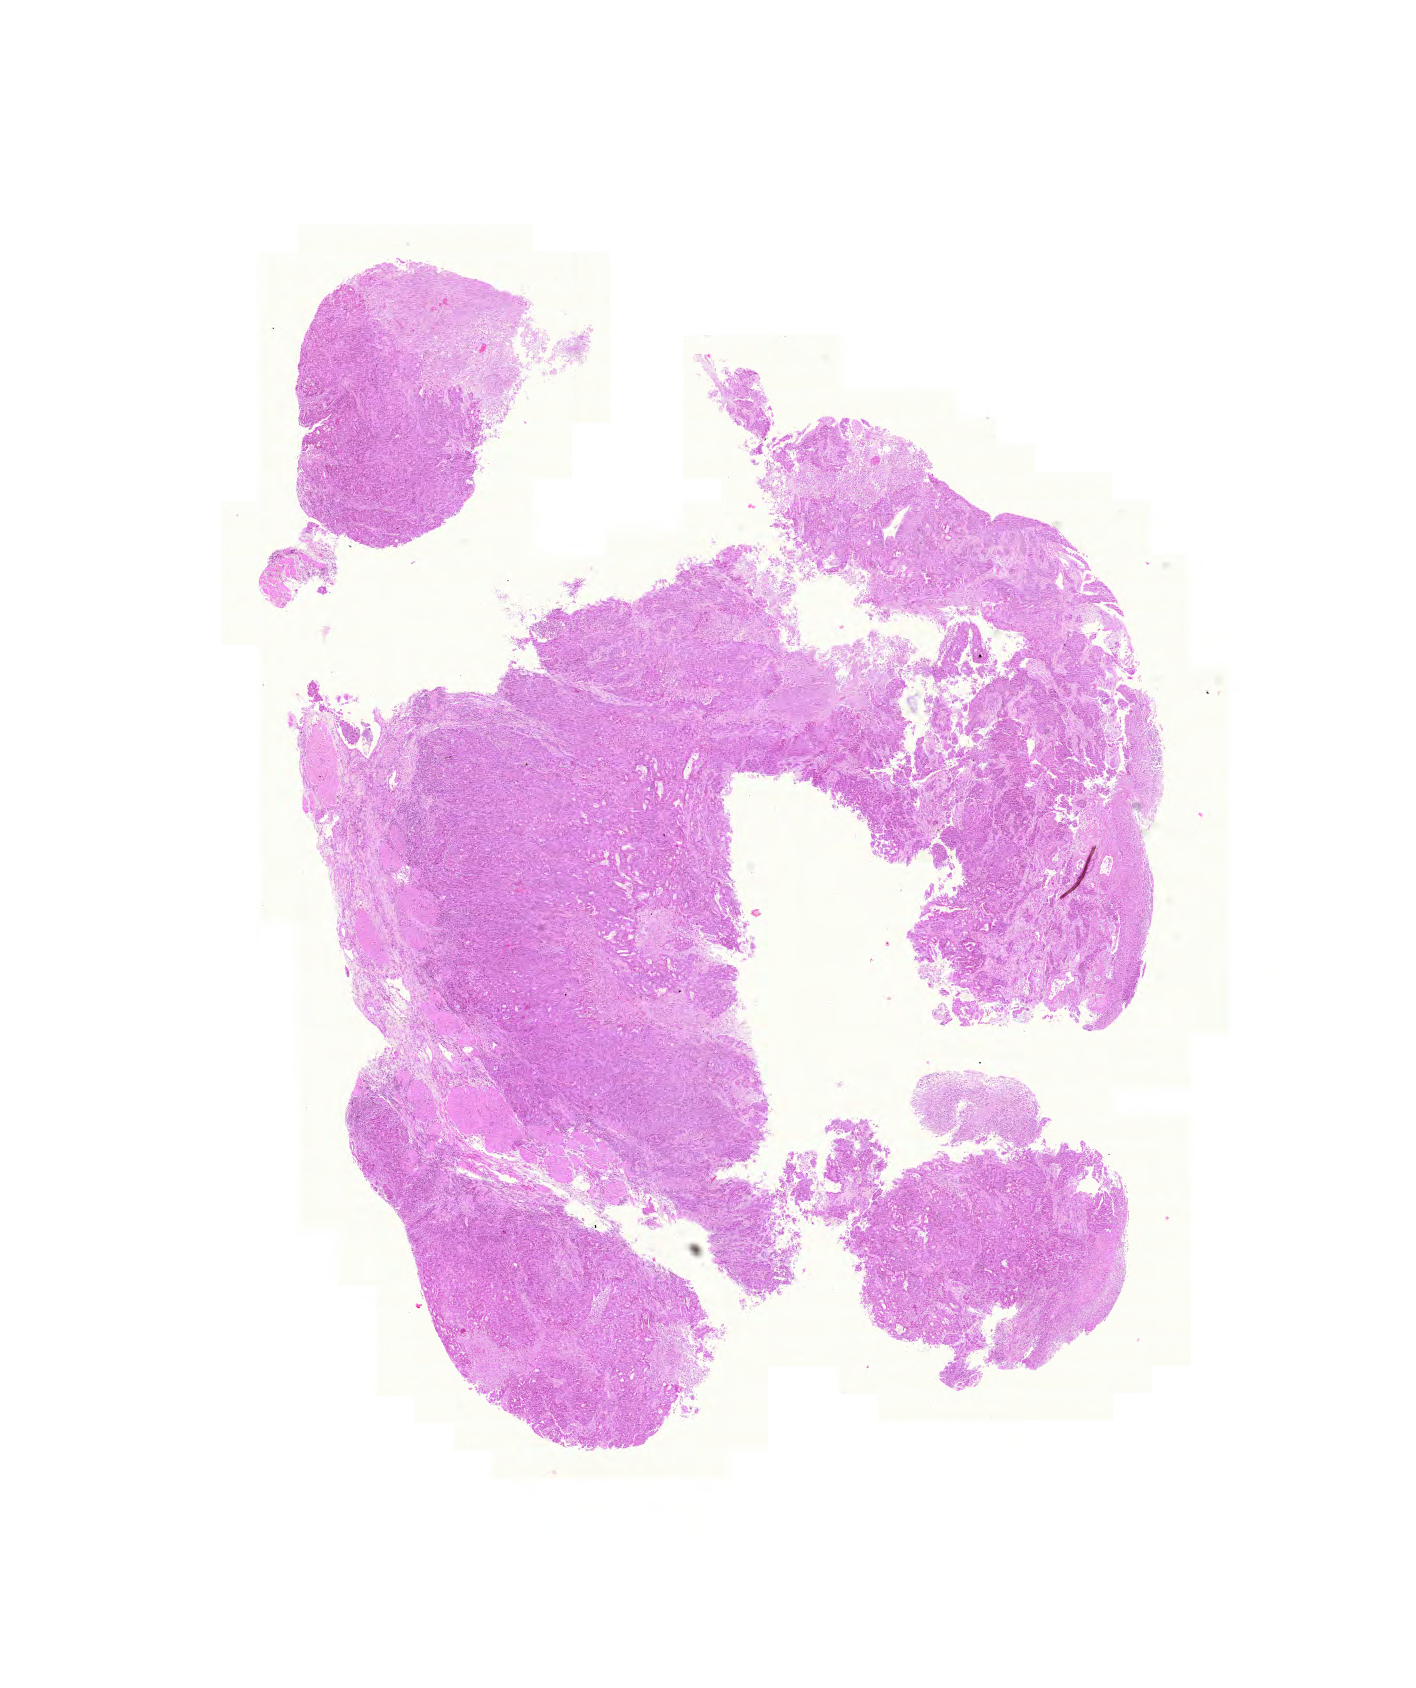
Digitized H&E tissue section (whole slide), whole scanned area (about 10.5 x 12.6 mm, slide scanned at 20x) shown as a low-resolution overview, formalin-fixed paraffin-embedded (FFPE) diagnostic section, stomach, primary tumour sample. Male, age 85 years at initial diagnosis. Histologic grade: G3 (poorly differentiated).
AJCC pathologic stage: IB. TNM: T2 N0 M0. Lymph nodes positive (case pathology): 0 of 27 examined. Diagnosis: Adenocarcinoma, intestinal type (gastric antrum).